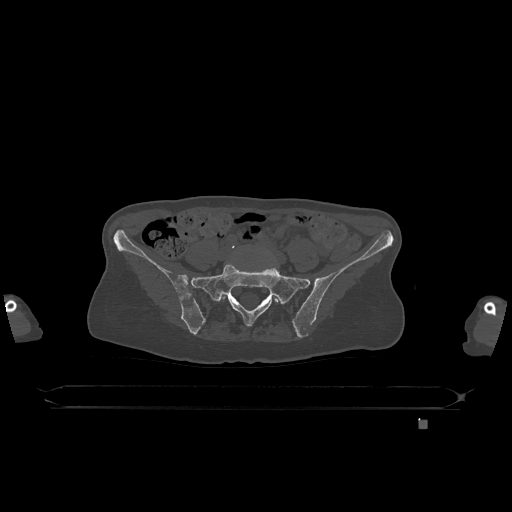
CT including the spine, one axial slice; position 199 of 1317 along the scan axis; bone window (W 1800 / L 400 HU); 0.5 mm slice thickness; 512 × 512 image matrix, field of view 500 × 500 mm. Female patient, age 74 years. From the clinical record (not read from this slice): primary cancer: lung; vertebrae with lytic lesions (as recorded): T1, T4, T5, T6, L4, L5.
Annotated regions visible in this slice (semi-automatically segmented with operator editing):
- L5 vertebra: bounding box (x1, y1, x2, y2) in pixels: (220, 294, 279, 303)